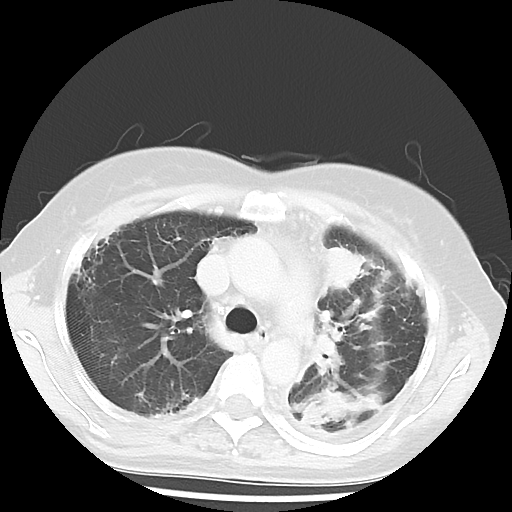
Chest CT, one axial slice. Position 39 of 56 along the scan axis. Reconstruction kernel LUNG. 120 kVp. Lung window (W 1500 / L -600 HU). 5 mm slice thickness. 512 × 512 image matrix, field of view 309 × 309 mm. Female patient, age 56 years. Case-level facts recorded for this patient, not image findings: clinical TNM (as recorded): T1c N0 M1.
Outlined on this slice (rectangle marked by the reading radiologist):
- lung tumour (recorded histology: adenocarcinoma): box from (x=319, y=243) to (x=365, y=296) px